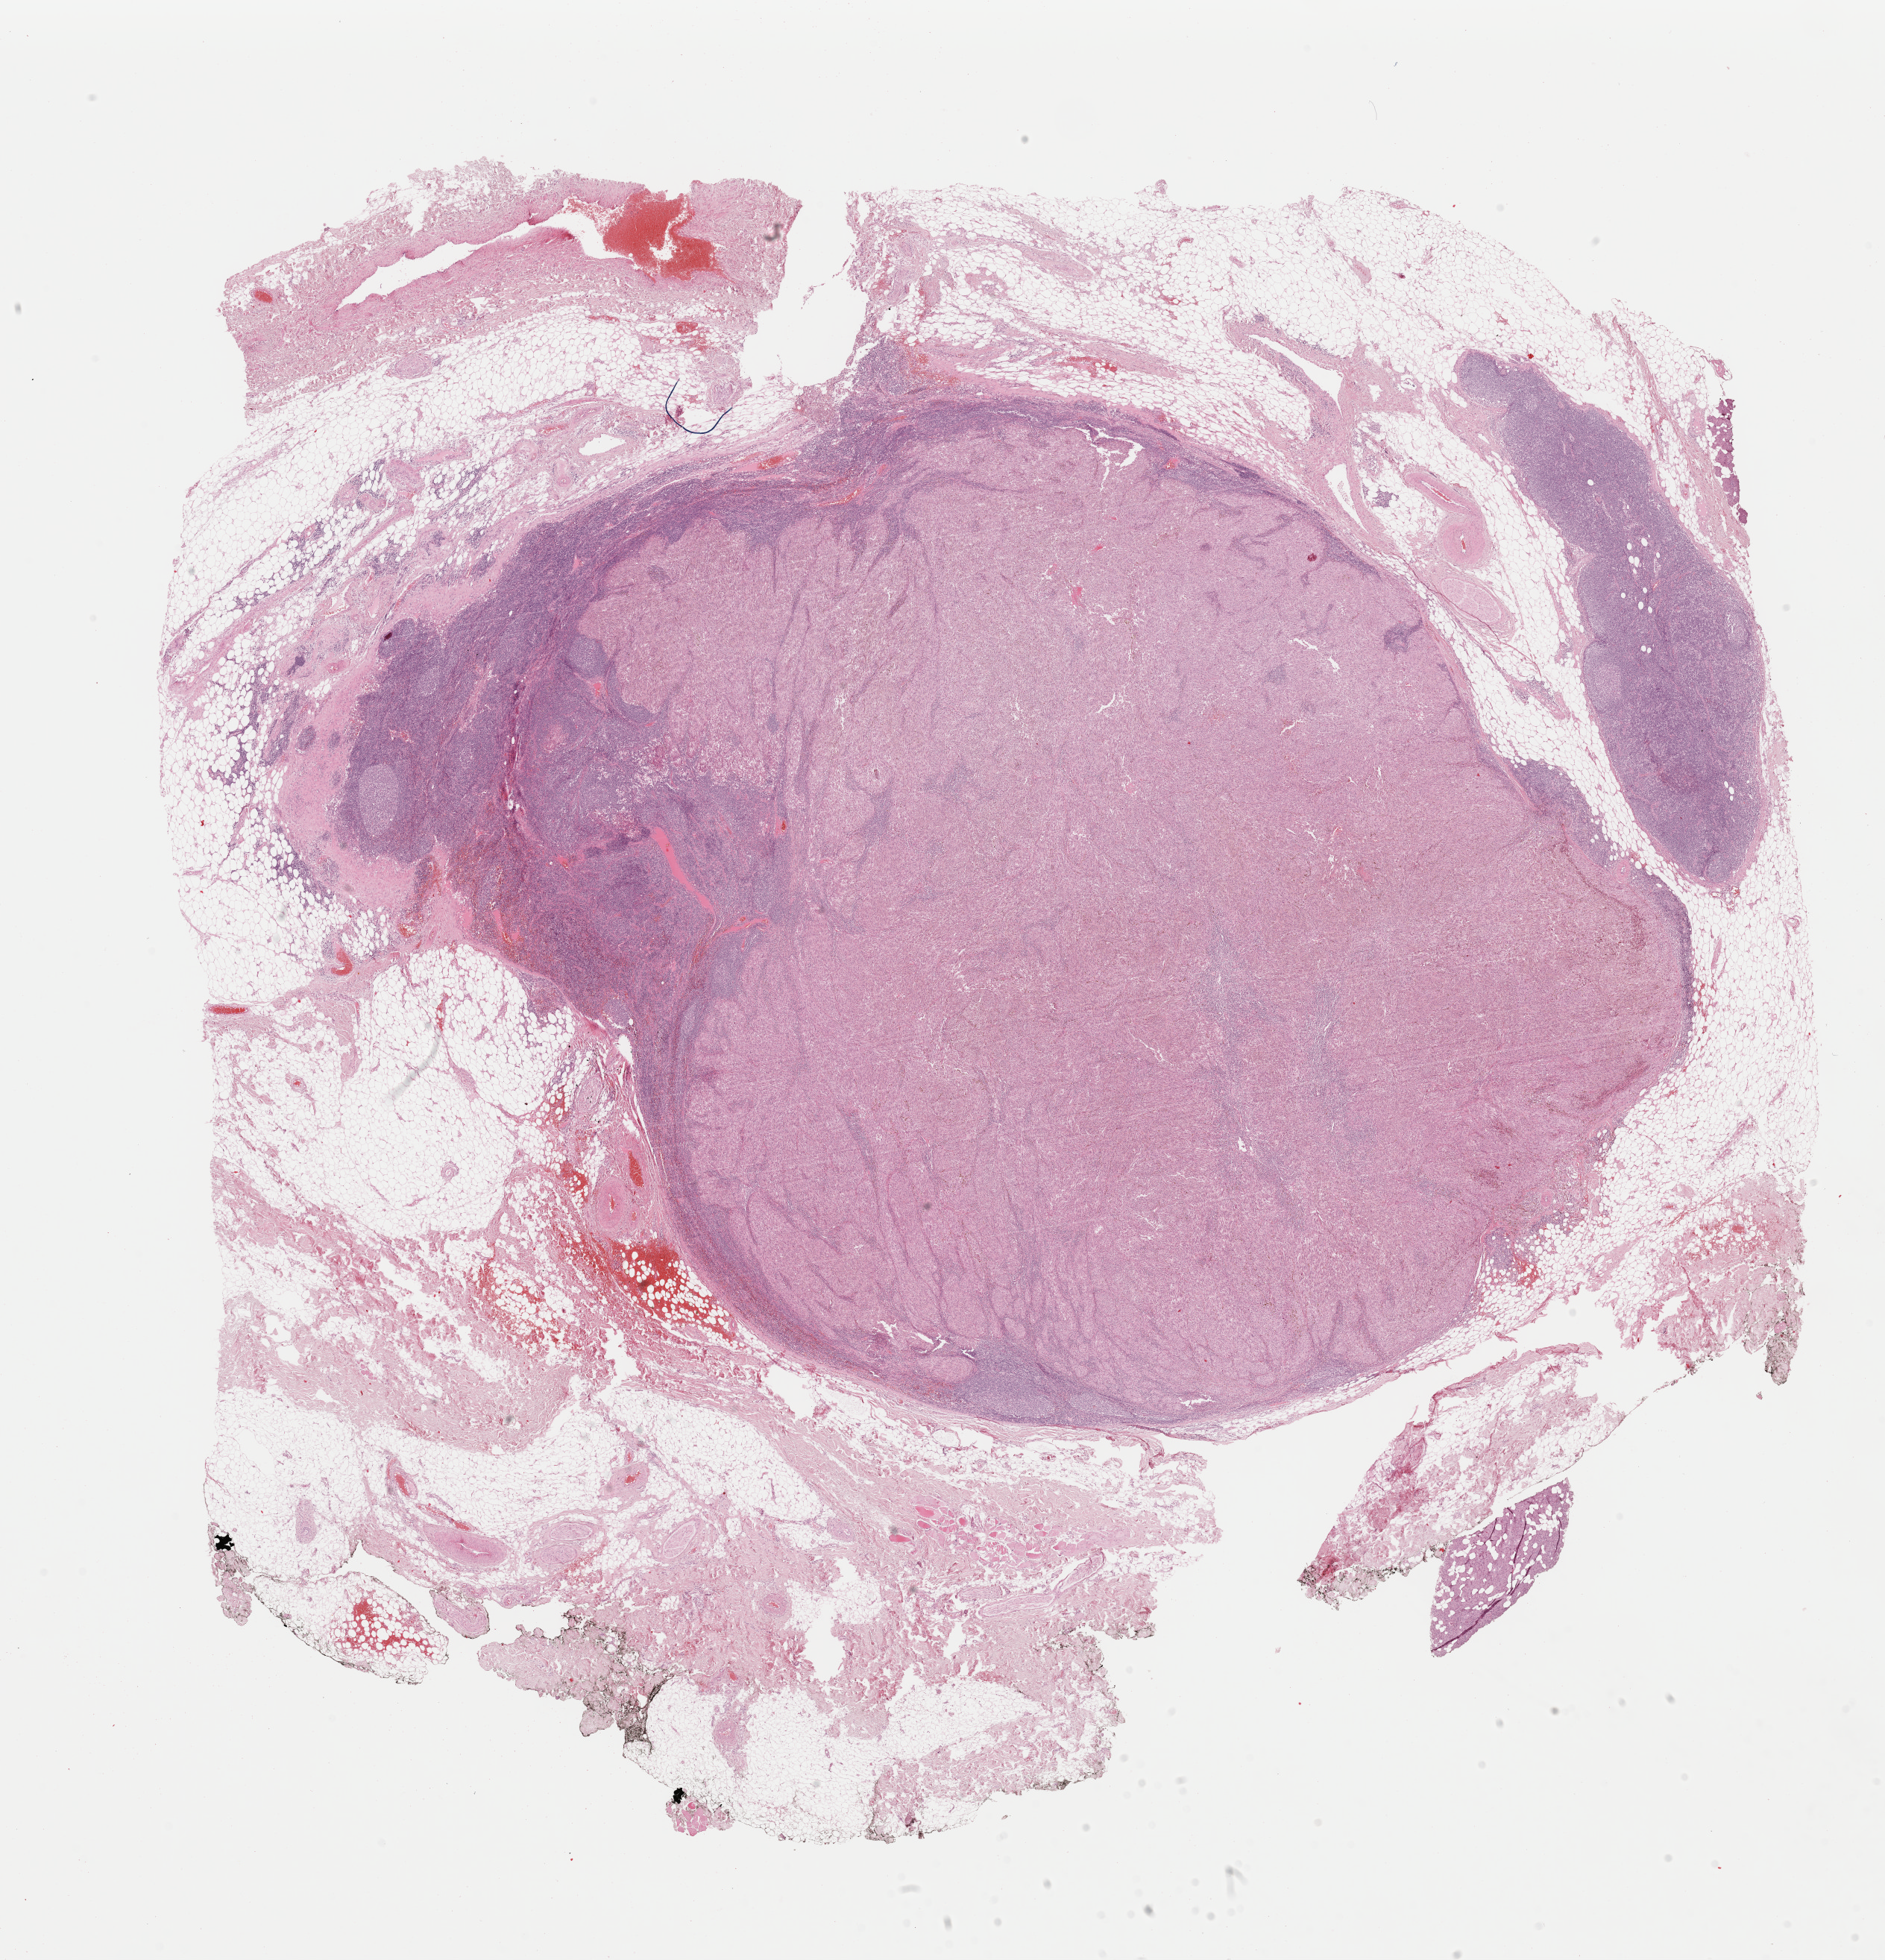
Hematoxylin and eosin (H&E) stained whole-slide image, a low-resolution overview of the entire scanned area, about 20.0 x 20.8 mm. Formalin-fixed paraffin-embedded (FFPE) diagnostic section. Metastatic tumour sample. Male, age 82 years at initial diagnosis.
• this section: metastatic tumour tissue
• patient diagnosis: Malignant melanoma, NOS